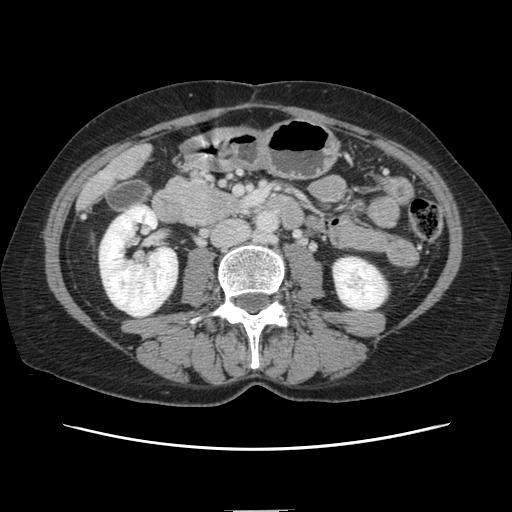
Contrast-enhanced abdominal CT, one axial slice; position 30 of 141 along the scan axis; intravenous contrast given; soft-tissue window (W 400 / L 40 HU); 512 × 512 image matrix. Female patient, age 63 years. From the clinical record (not read from this slice): diagnosis: colorectal cancer liver metastases, imaged before liver resection; multiple liver metastases: yes; largest metastasis: 3.2 cm; disease in both lobes: yes.
Structures marked on this image (outlined manually by an expert reader):
- liver: box from (x=81, y=146) to (x=150, y=205) px